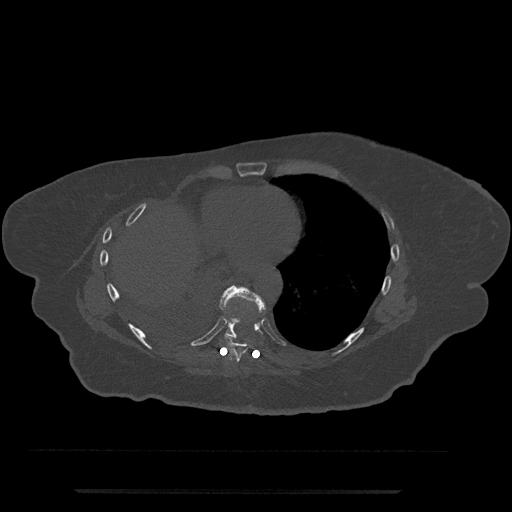
CT including the spine, one axial slice. Slice 369 of 797 in the series (ordered by position). Bone window (W 1800 / L 400 HU). 0.5 mm slice thickness. 512 × 512 image matrix, field of view 440 × 440 mm. Patient: female, 51 years. From the clinical record (not read from this slice): primary cancer: neuro.
Structures marked on this image (semi-automatic segmentation, software-assisted and operator-edited):
- T8 vertebra: box from (x=224, y=334) to (x=248, y=362) px
- T9 vertebra: (x=218, y=285)–(x=266, y=339)